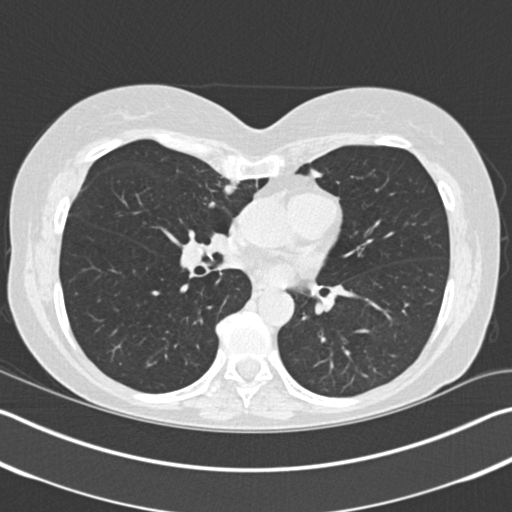
Chest CT (low-dose screening protocol), one axial image; first (baseline) screen; lung window (W 1500 / L -600 HU); 2 mm slice thickness; 120 kVp; 512 × 512 image matrix. Female participant, aged 61 years at enrolment. Former smoker at enrolment.
Expert reader's lesion annotation, bounding box (x1, y1, x2, y2) in pixels: (199, 168, 251, 213). The screening reader recorded 2 non-calcified nodules or masses ≥4 mm on this exam (right upper lobe, right upper lobe); which of them this box marks is not recorded.